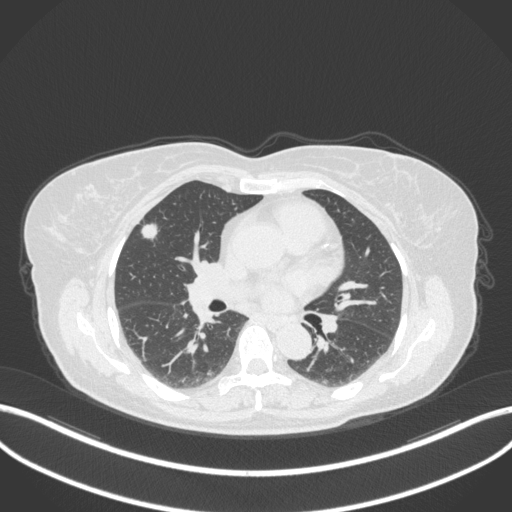
Chest CT, one axial slice. Slice 180 of 310 in the series (ordered by position). Reconstruction kernel B31f. 120 kVp. Lung window (W 1500 / L -600 HU). 1 mm slice thickness. 512 × 512 image matrix, field of view 400 × 400 mm. Patient: female, 55 years. From the clinical record (not read from this slice): clinical TNM (as recorded): T1b N0 M0.
Structures marked on this image (bounding box drawn by a radiologist):
- lung tumour (recorded histology: adenocarcinoma): bounding box (x1, y1, x2, y2) in pixels: (137, 218, 163, 245)